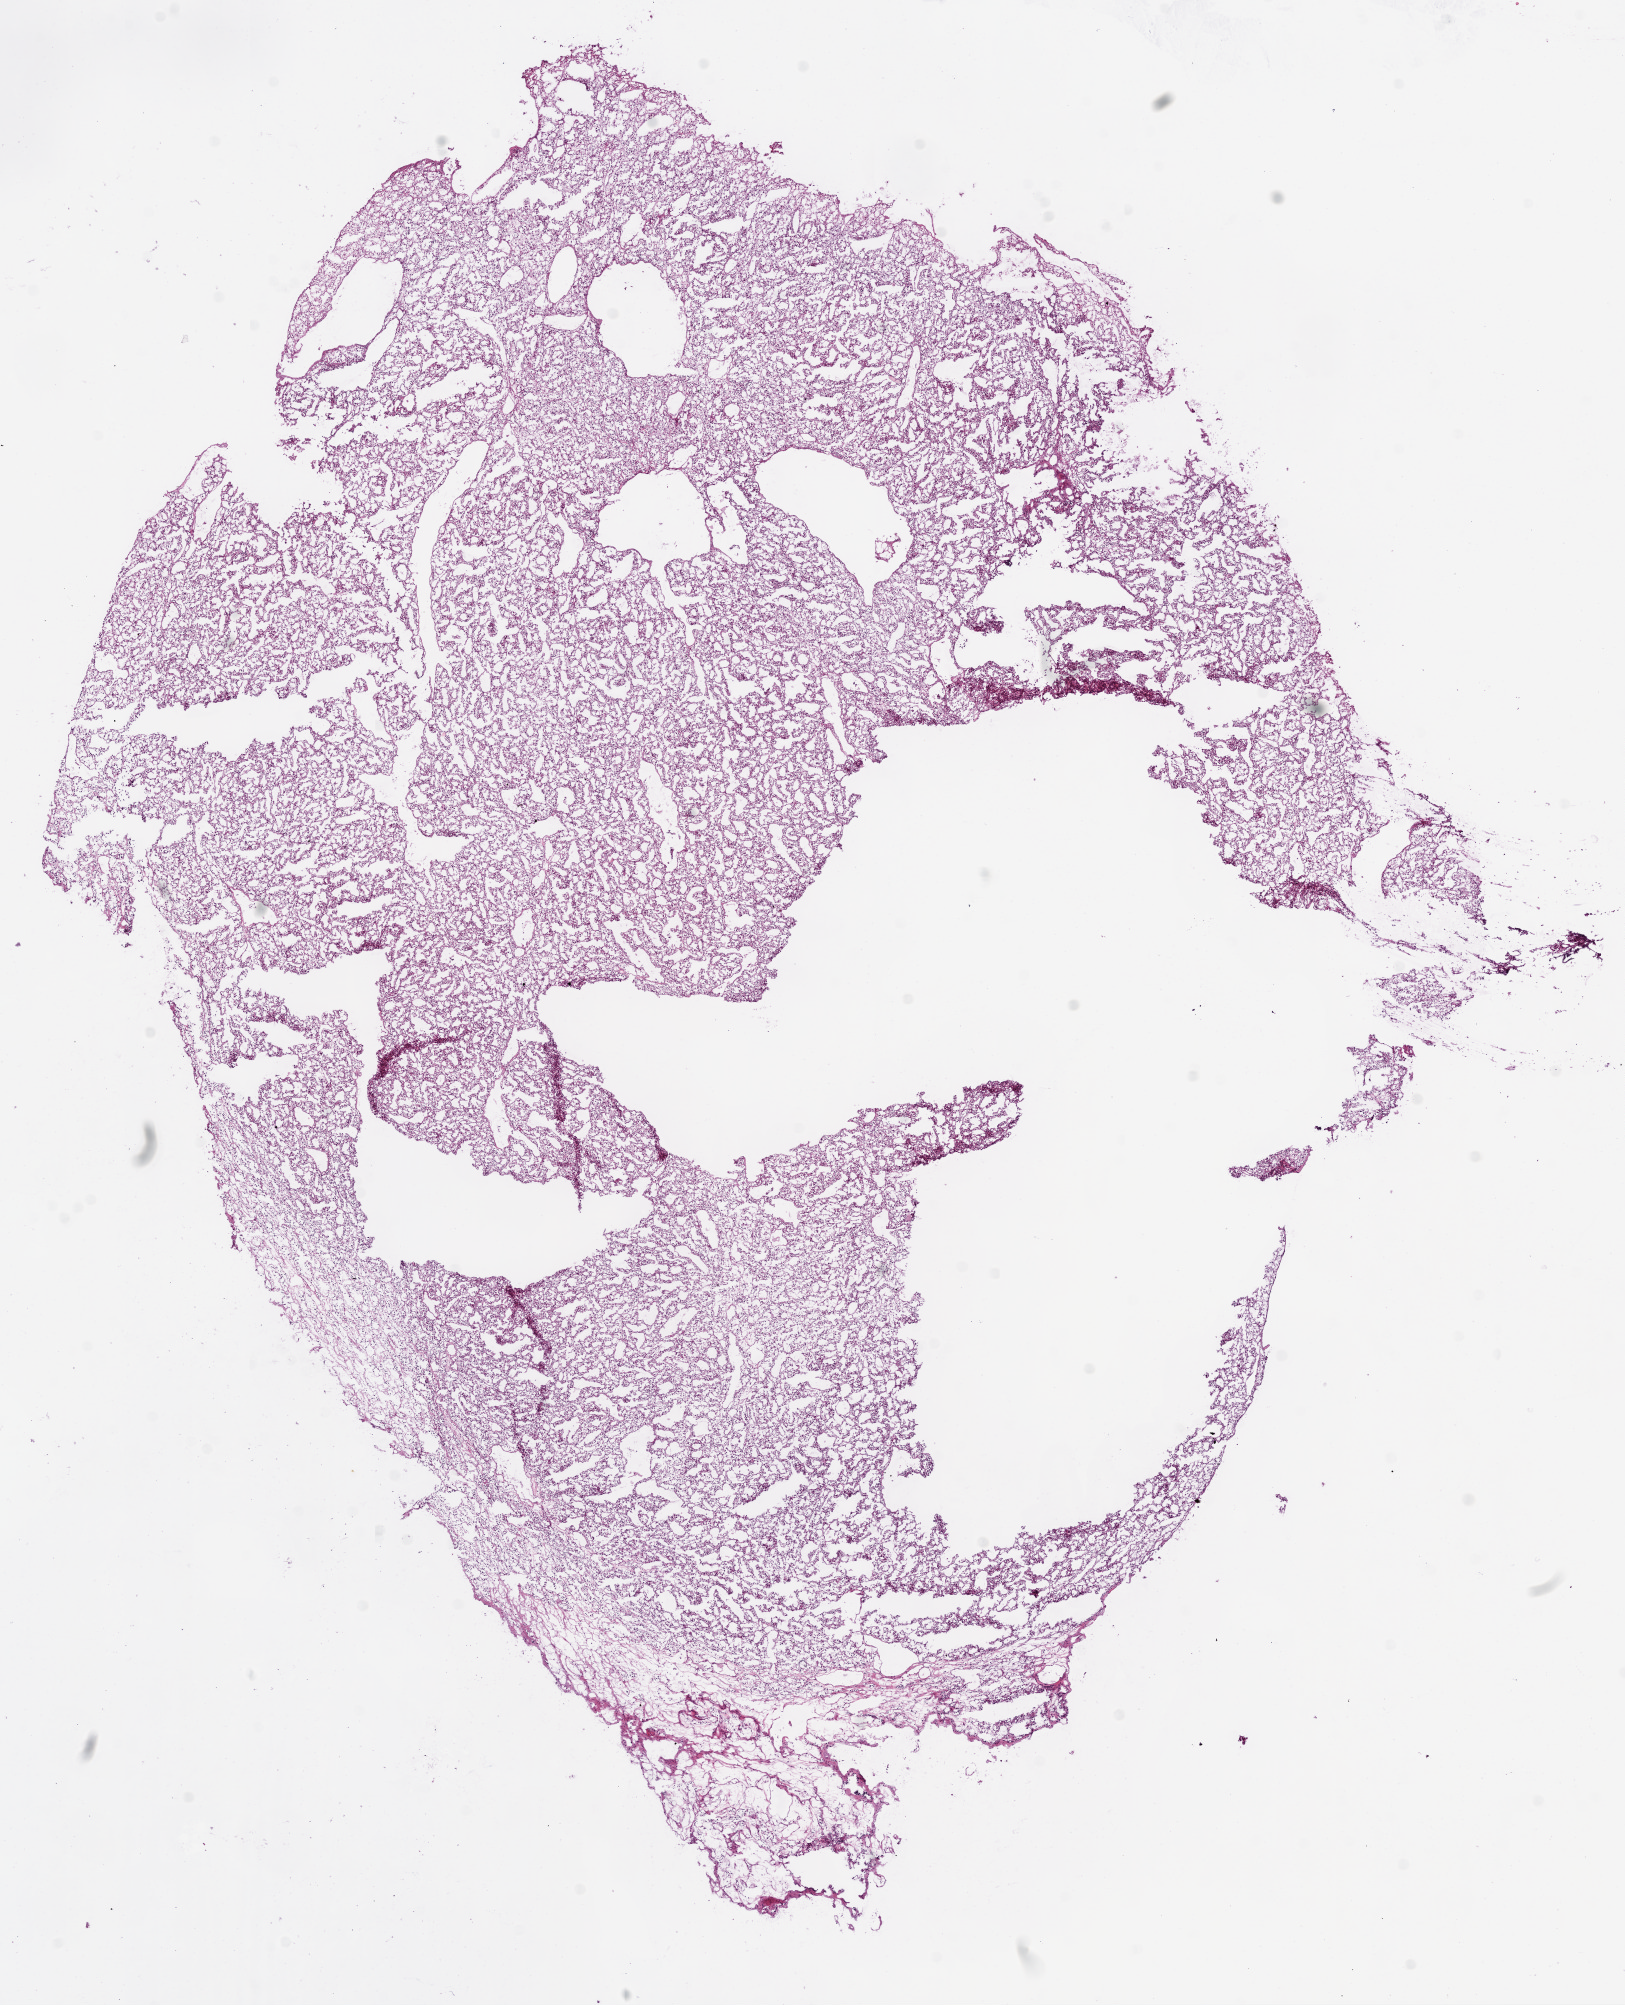
Hematoxylin and eosin (H&E) stained whole-slide image — a low-resolution overview of the entire scanned area, about 13.0 x 16.1 mm, frozen section from the bottom of the tissue portion, primary tumour sample from the kidney. Female, age 51 years at initial diagnosis. Histologic grade: G2 (moderately differentiated). Pathologist review of this section (percent, as recorded): tumour cells 95%, tumour nuclei 90%, normal cells 0%, stromal cells 5%, necrosis 0%.
AJCC pathologic stage: III. Diagnosis: Clear cell adenocarcinoma, NOS. TNM: T3a NX M0.